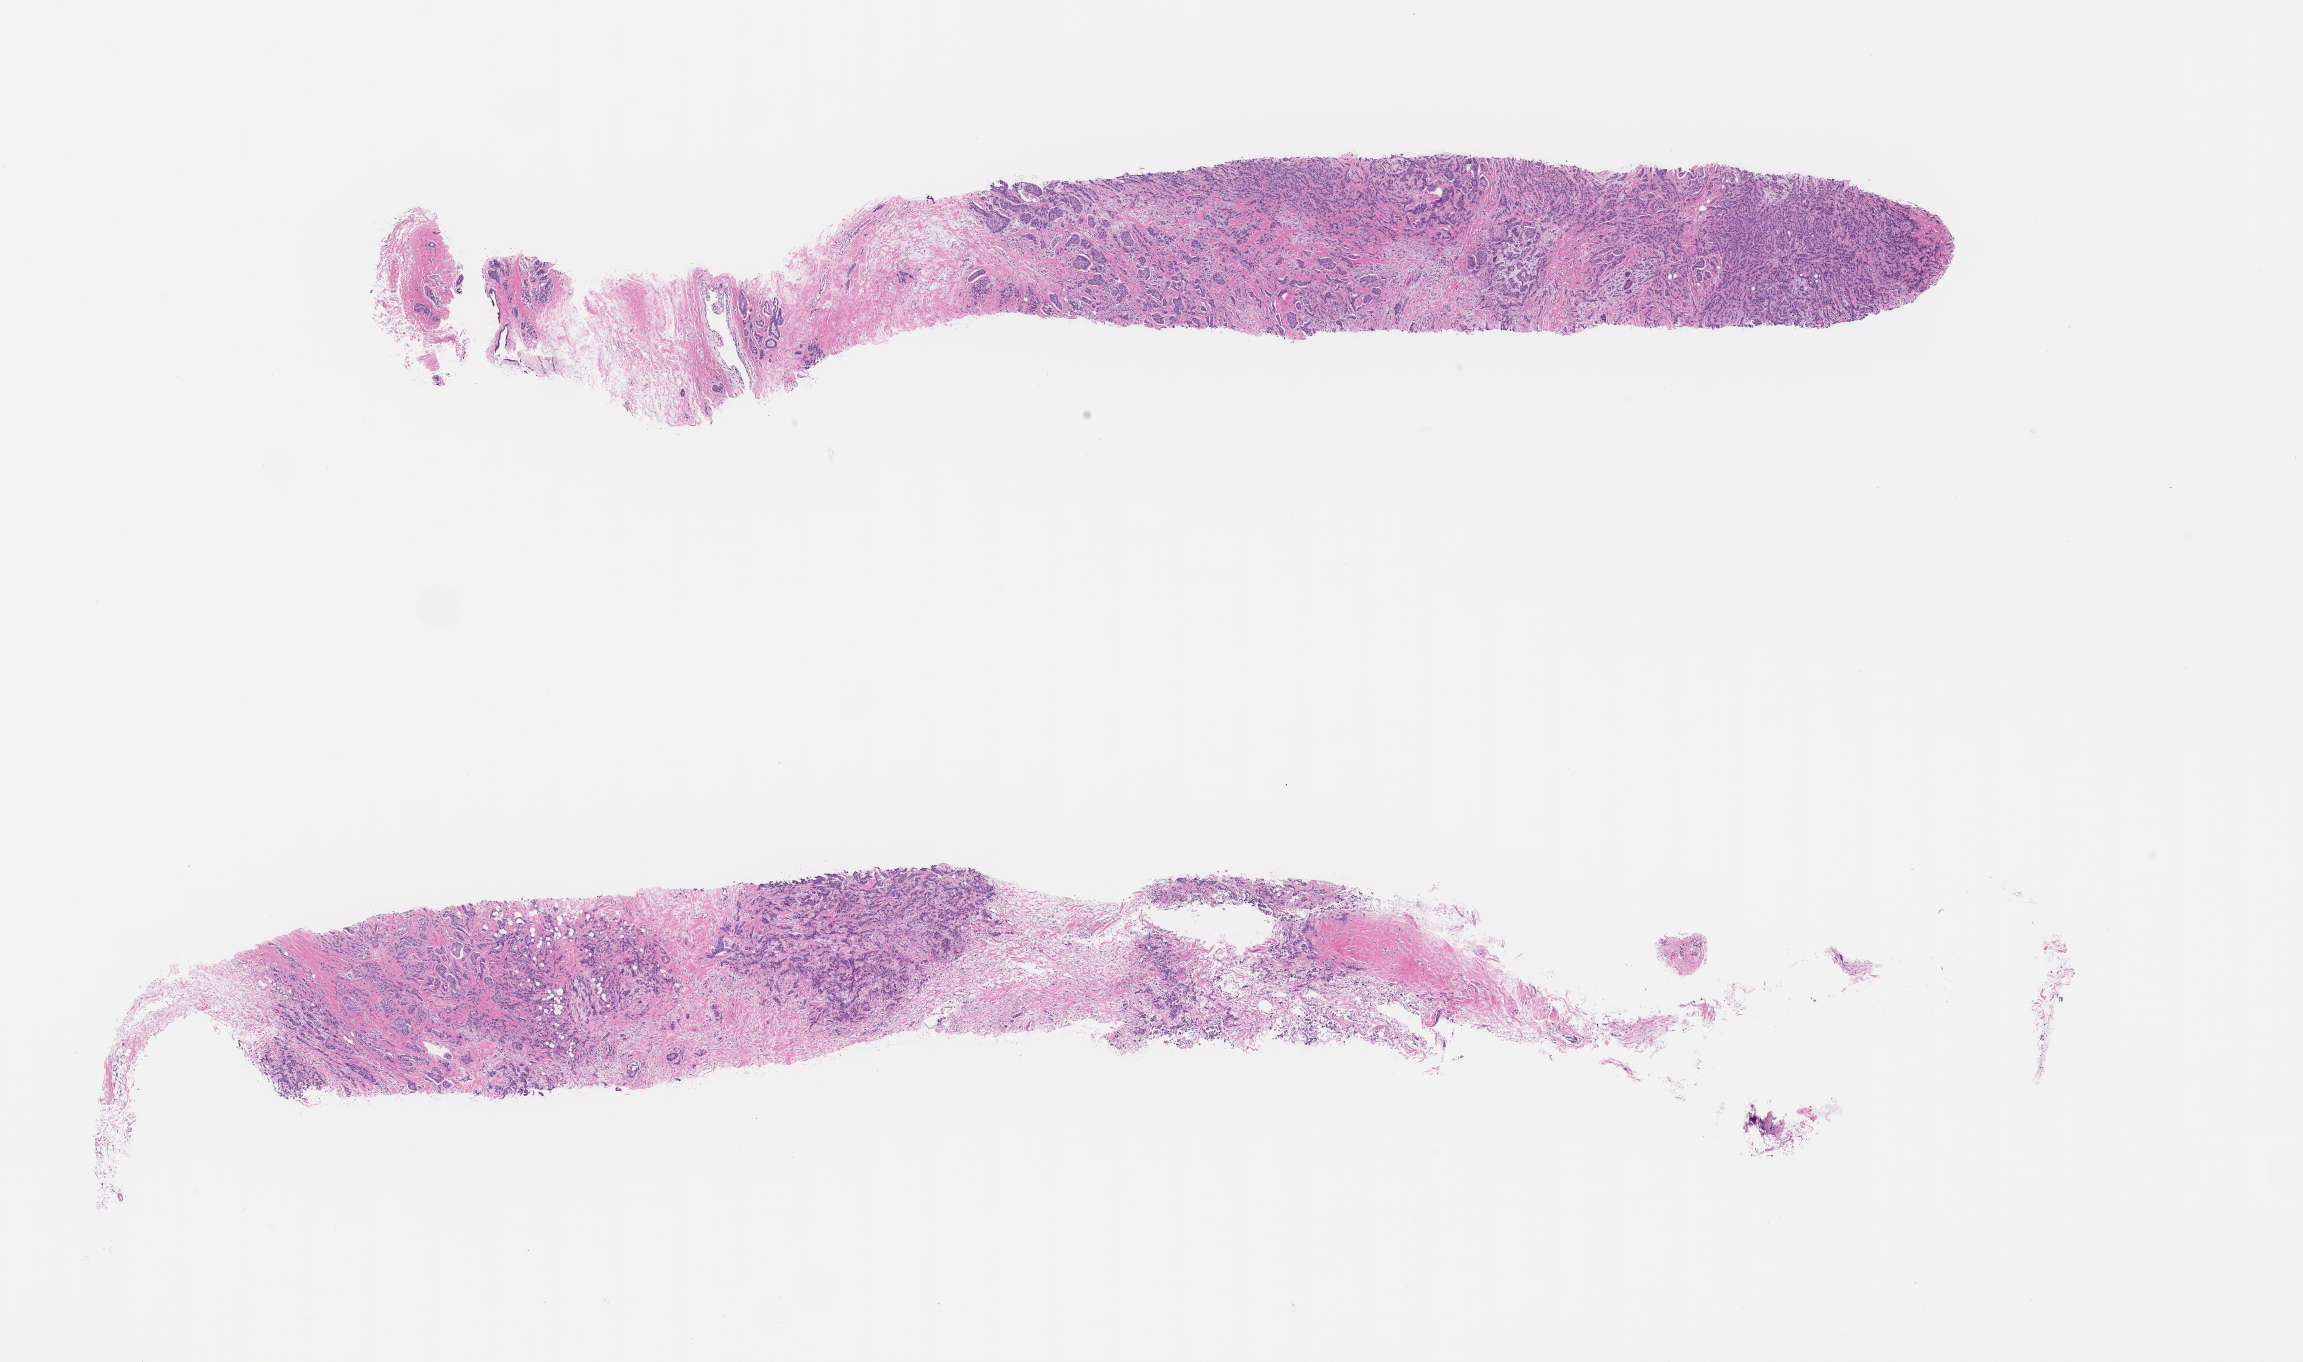
Hematoxylin and eosin (H&E) whole-slide image — a low-resolution overview of the entire scanned area, about 18.6 x 11.0 mm; formalin-fixed, paraffin-embedded (FFPE) tissue; tissue site: breast; archival tissue. Patient: female.
• this section: primary tumor
• diagnosis: Invasive Breast Carcinoma